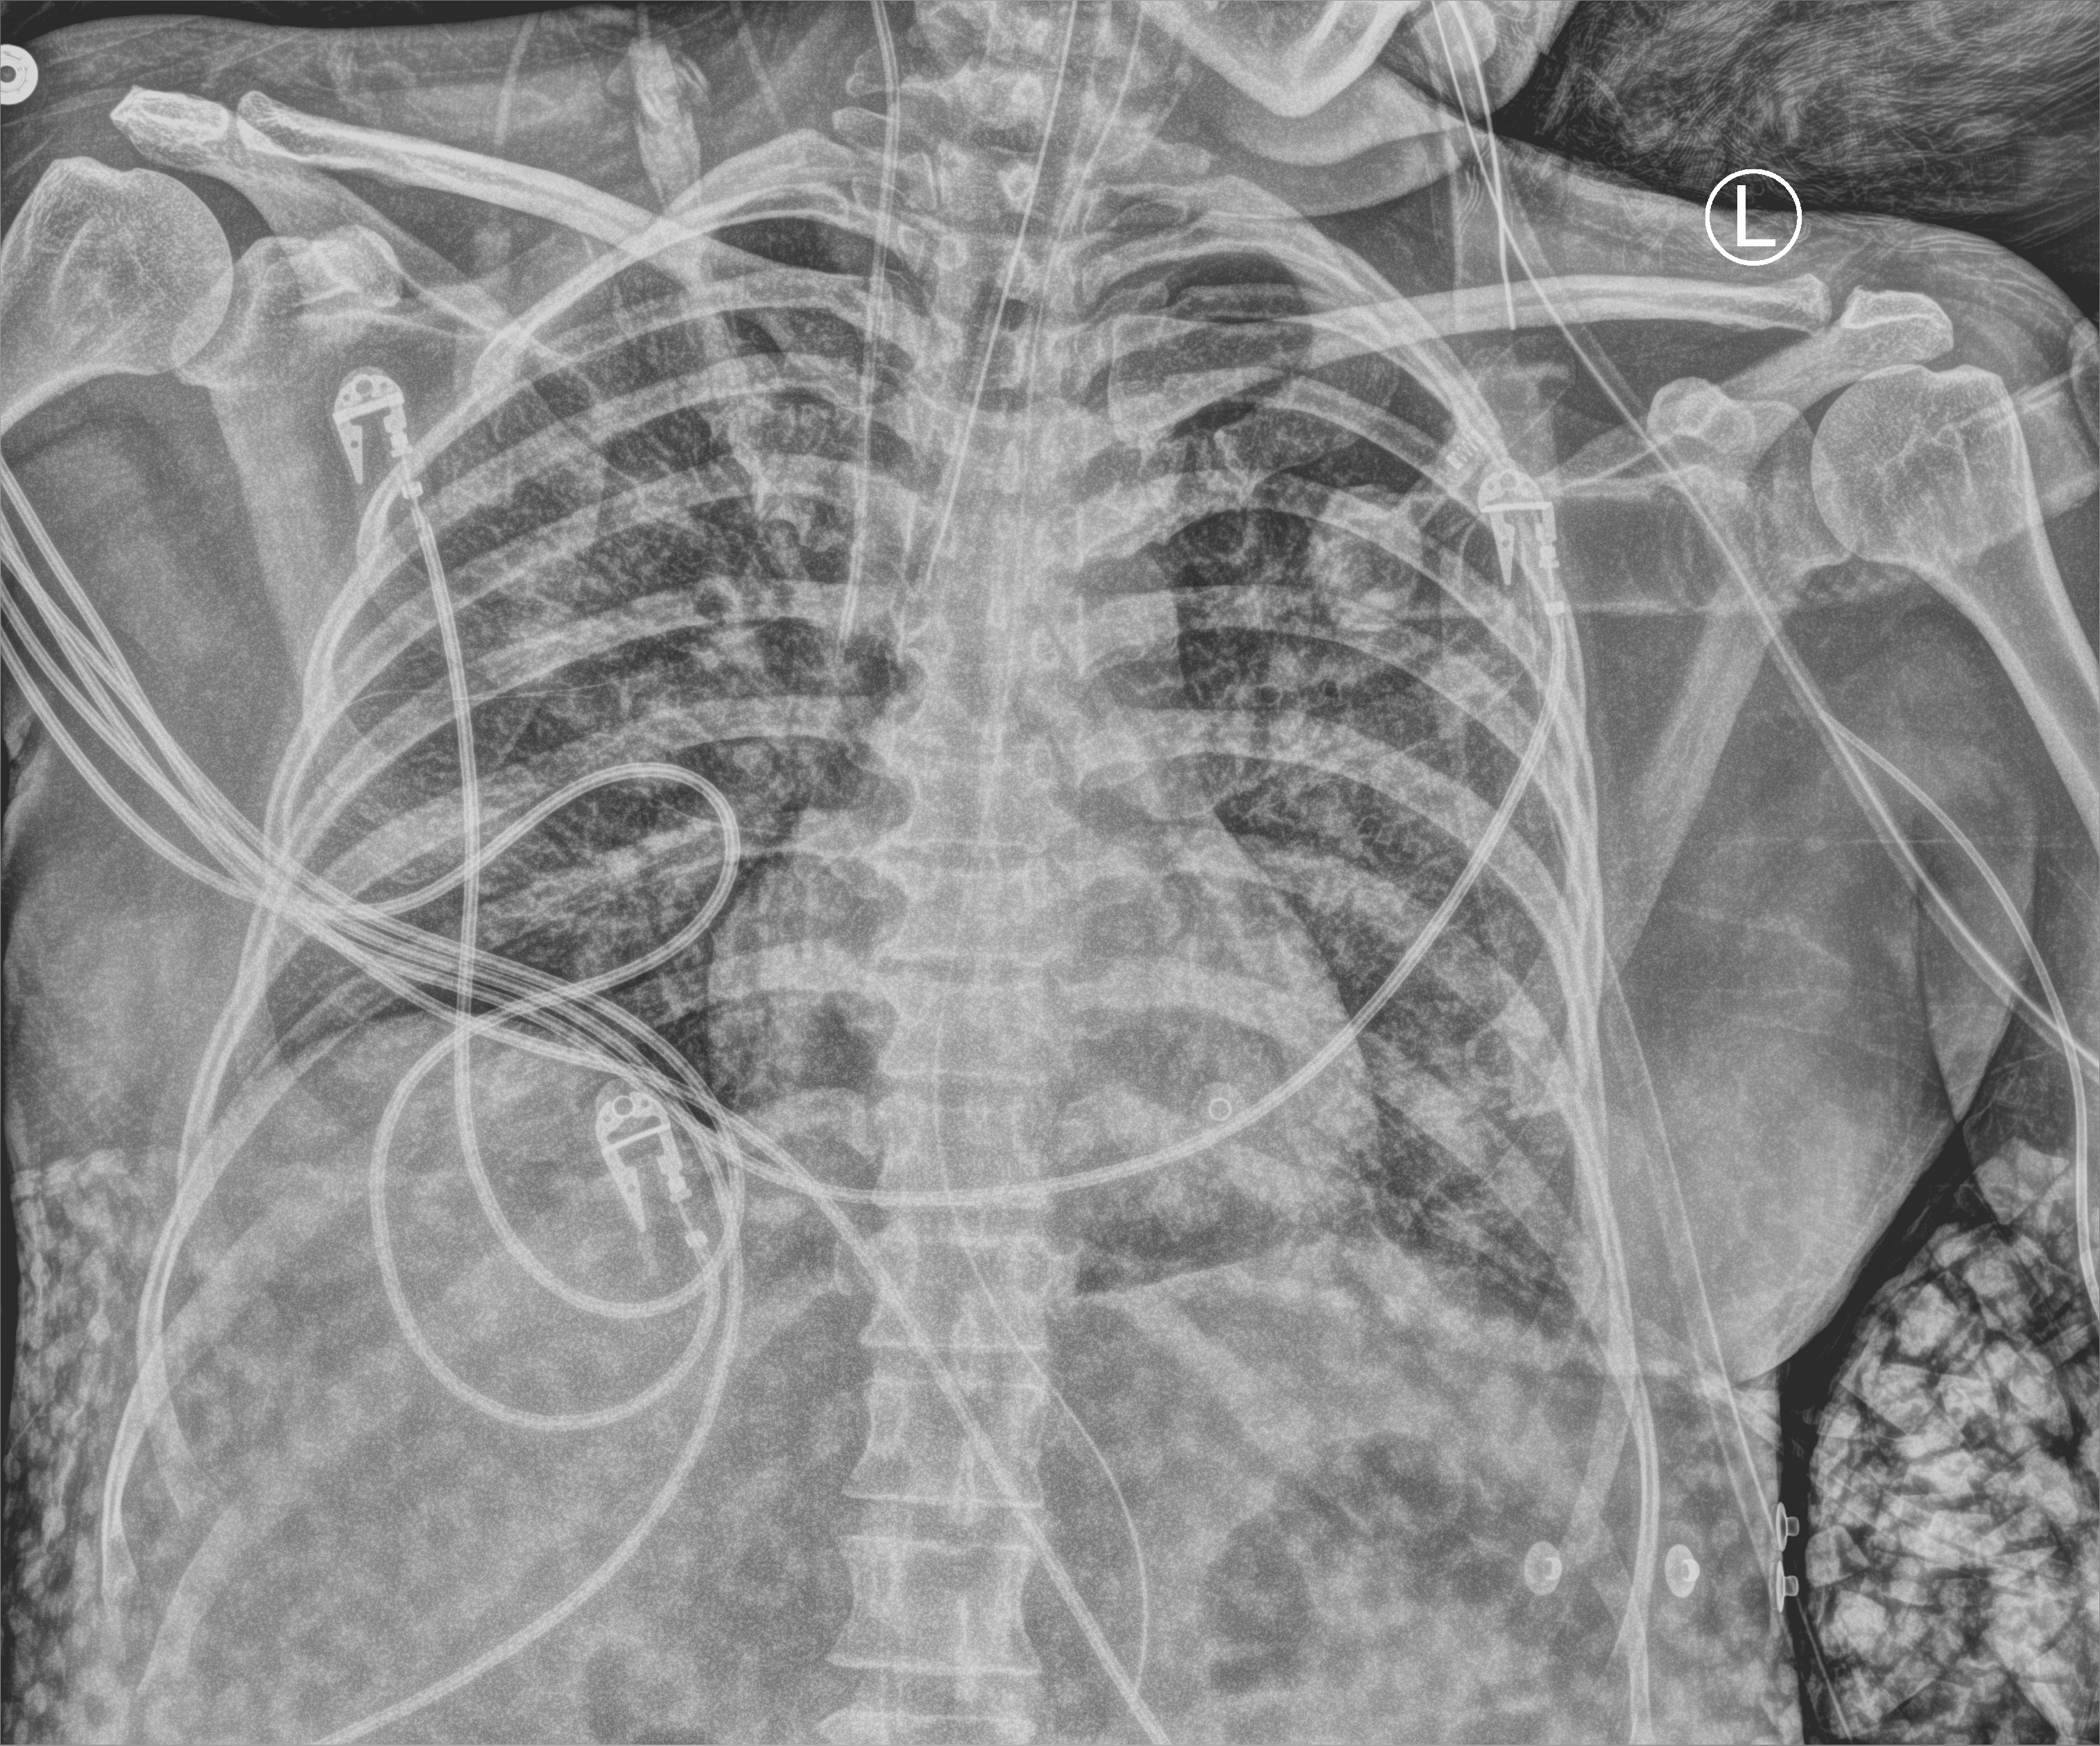
Portable chest radiograph; anteroposterior (AP) projection. Patient hospitalised with COVID-19; female, aged 18–59 years.
Admission-level facts for this patient (not findings on this image; timing relative to this image not recorded): smoking status (admission record): former; mechanically ventilated during this hospital stay: yes; admitted to intensive care during this hospital stay: yes.